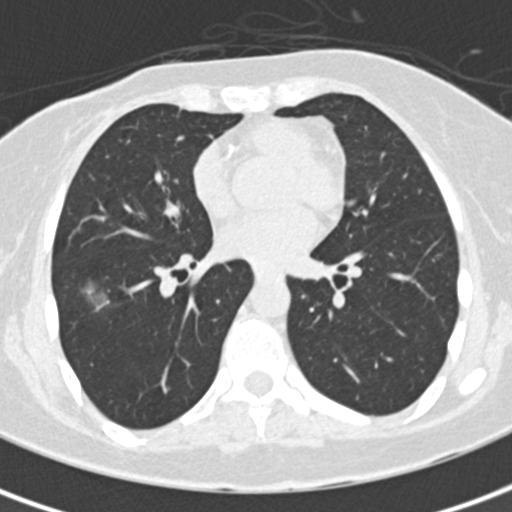
Low-dose screening chest CT, one axial slice. 120 kVp. Lung window (W 1500 / L -600 HU). 2 mm slice thickness. 512 × 512 image matrix, field of view 284 × 284 mm.
Structures marked on this image (outlined manually by an expert reader):
- lesion 1 (tumor, lower lobe of right lung): box from (x=83, y=279) to (x=110, y=311) px